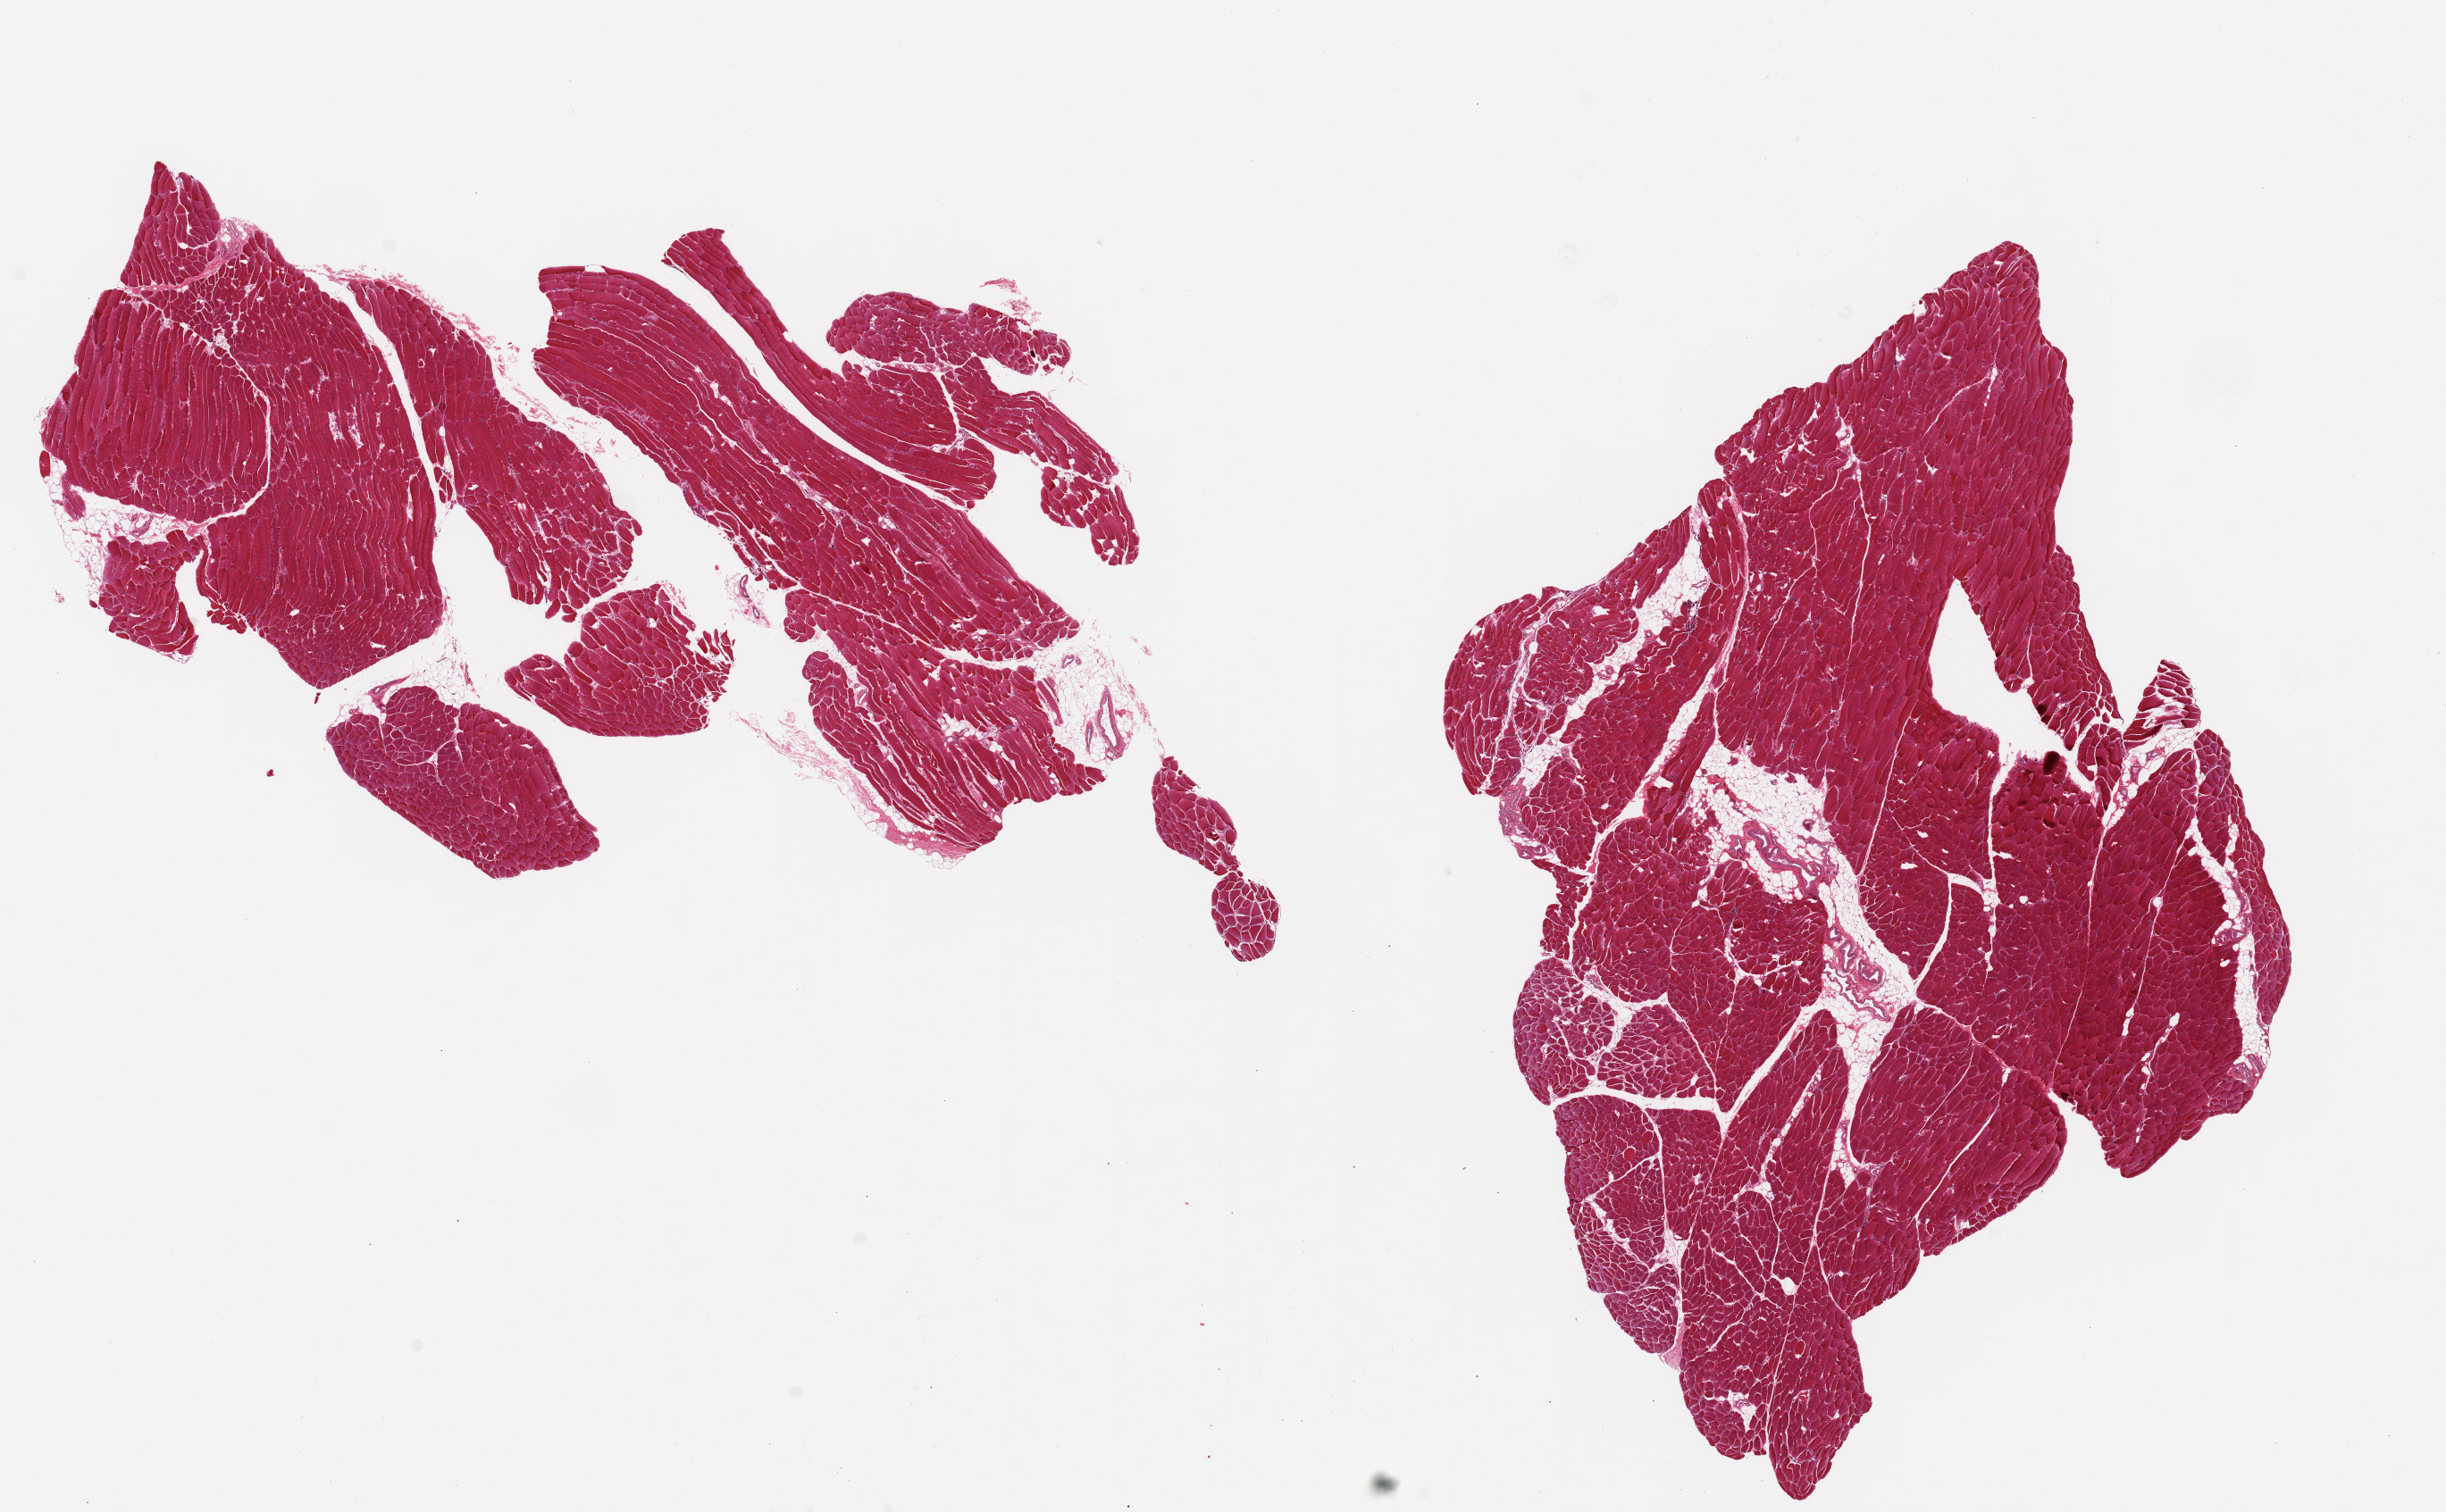
Haematoxylin and eosin whole-slide image — whole scanned area (about 21.7 x 13.4 mm) shown as a low-resolution overview, PAXgene-fixed, paraffin-embedded tissue, target tissue: skeletal muscle, tissue donor sample. Donor: male.
Pathologist's review note for this sample: 2 pieces, ~10-15% interstitial fat.